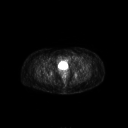
FDG PET of an extremity soft-tissue mass (from a PET/CT study), one axial slice; position 56 of 267 along the scan axis; 128 × 128 image matrix, field of view 700 × 700 mm. Female patient, age 47 years. From the clinical record (not read from this slice): histological type: myxofibrosarcoma; grade: intermediate; site of the primary tumour: left thigh.
Structures marked on this image (expert contour drawn on MRI and transferred to this co-registered scan by the dataset authors):
- gross tumour volume including surrounding oedema: bounding box (x1, y1, x2, y2) in pixels: (67, 58, 82, 63)